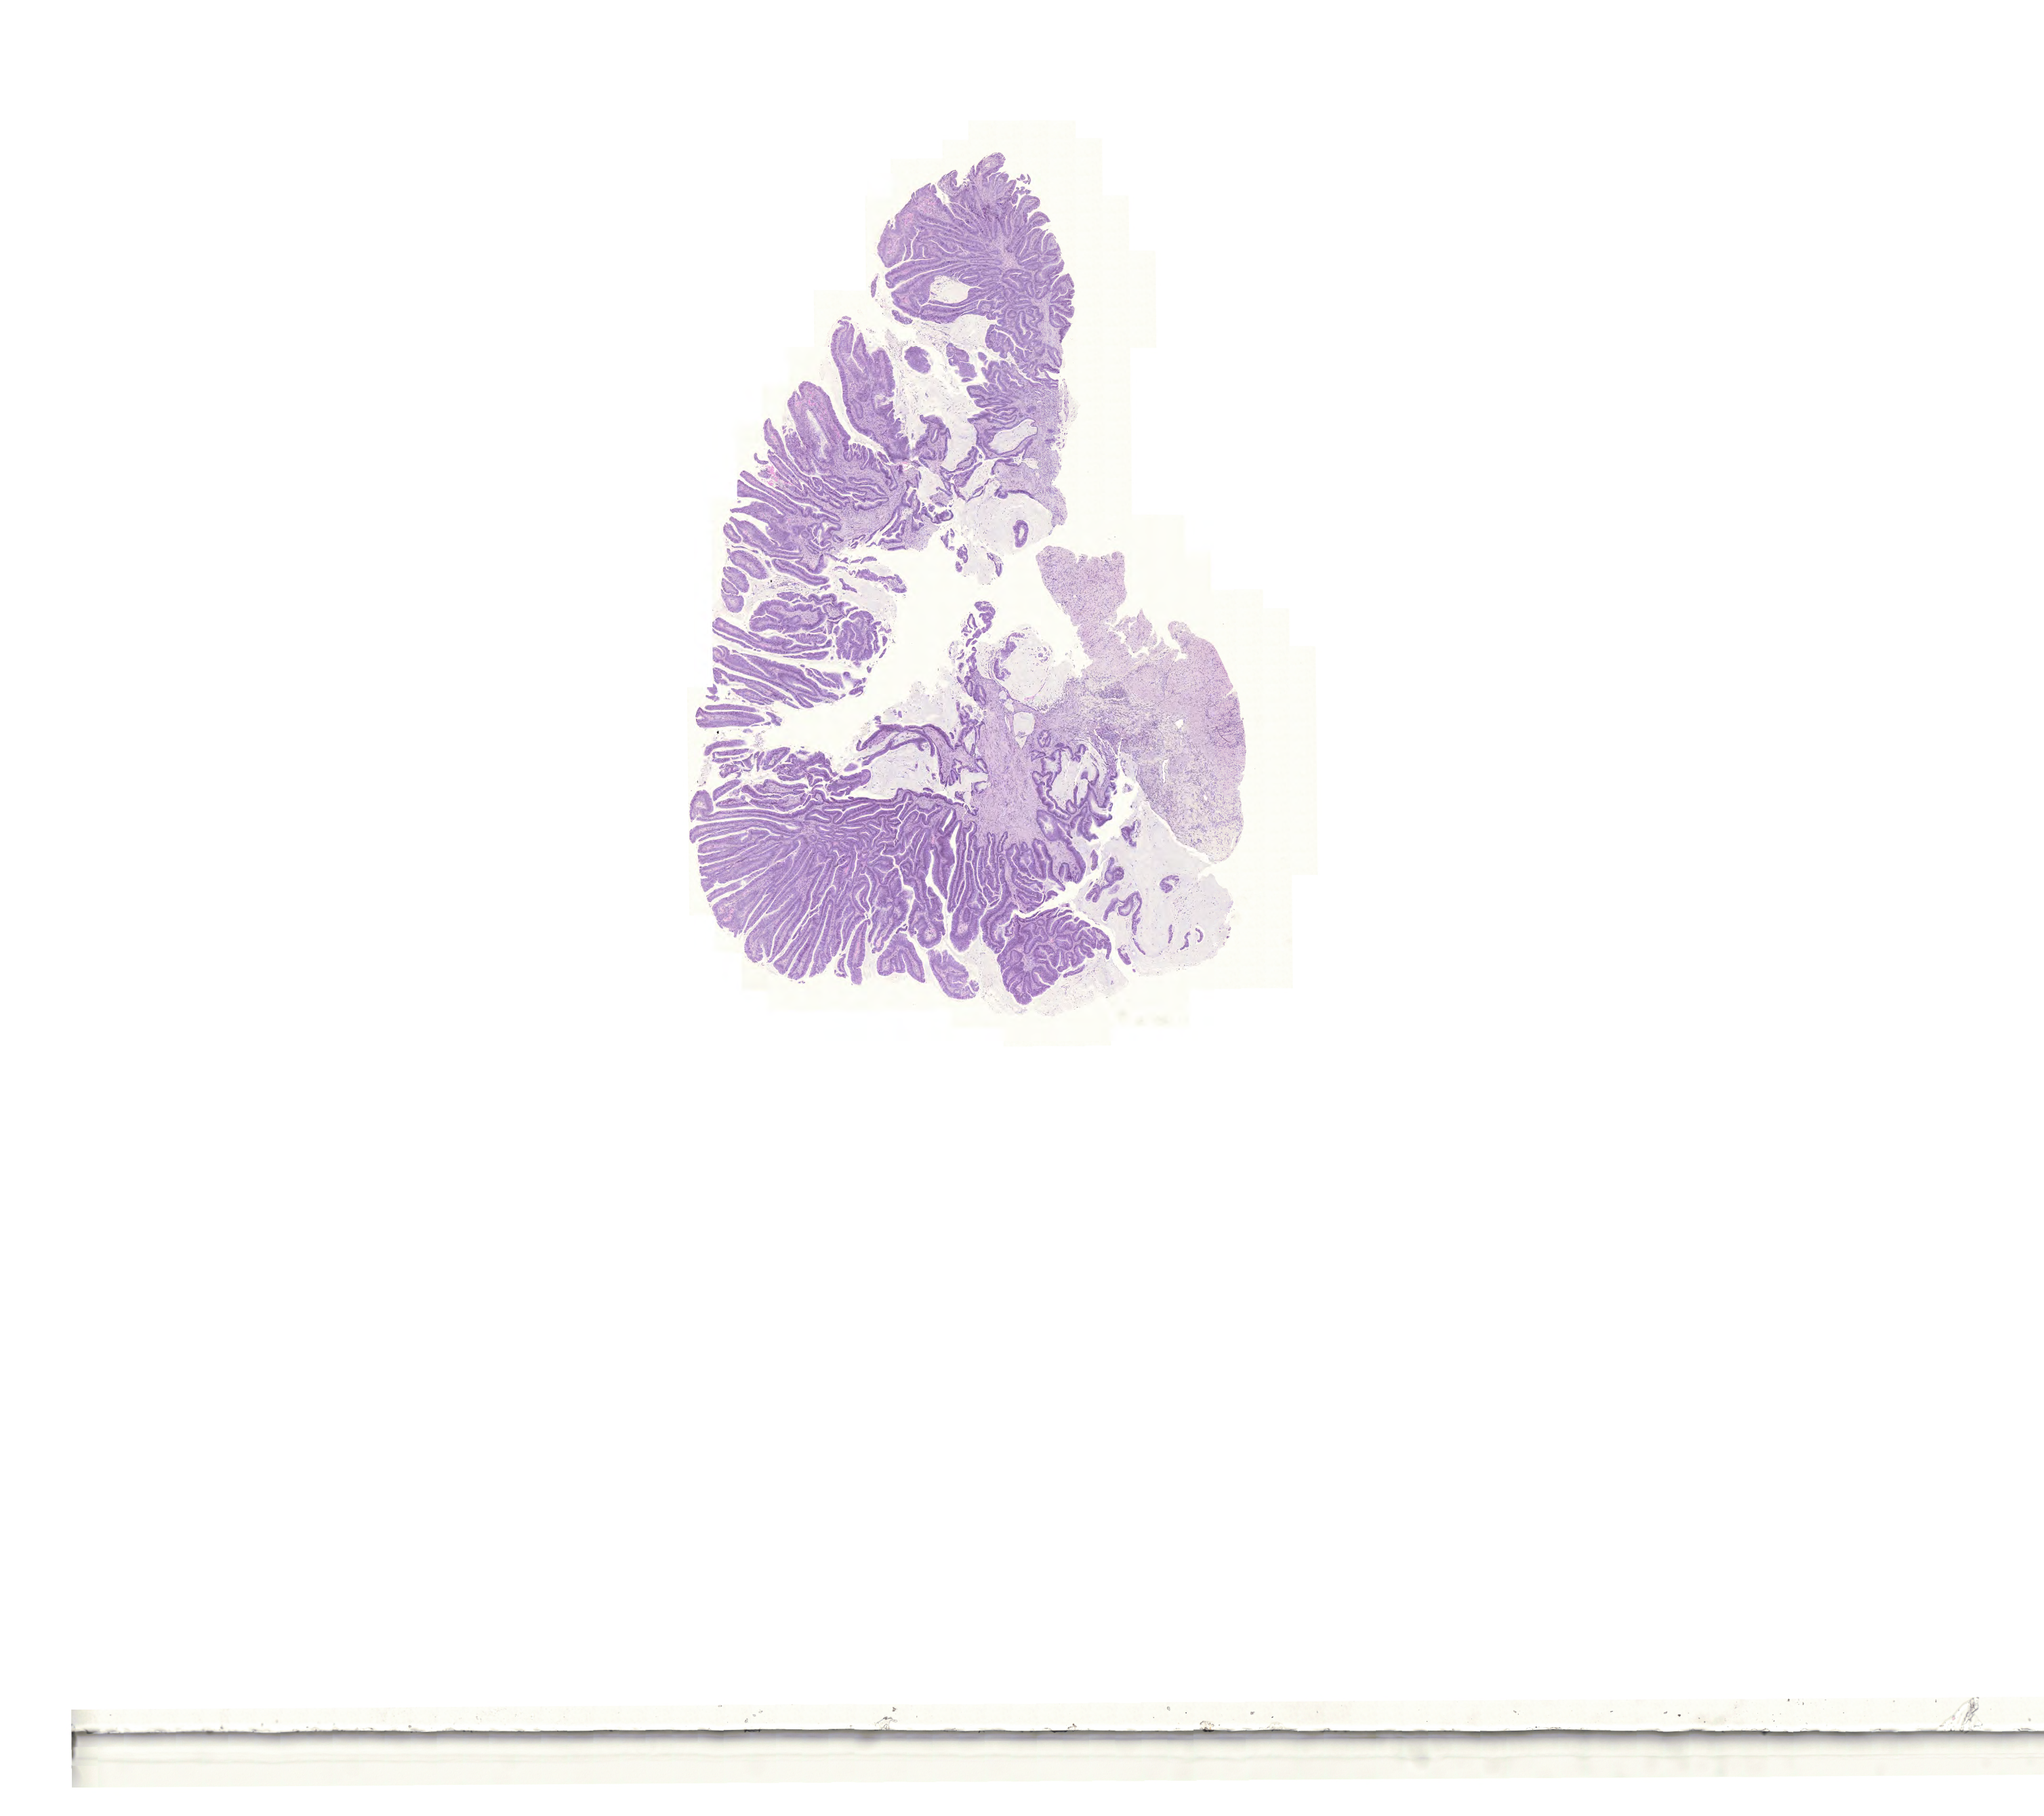
Whole-slide histology image, H&E — whole scanned area (about 22.4 x 19.9 mm) shown as a low-resolution overview, formalin-fixed paraffin-embedded (FFPE) diagnostic section, sample: primary tumour, colon. Patient: female, age at initial diagnosis 81 years.
TNM: T2 N0 M0. Histologic diagnosis: Mucinous adenocarcinoma (ascending colon). AJCC pathologic stage: I.